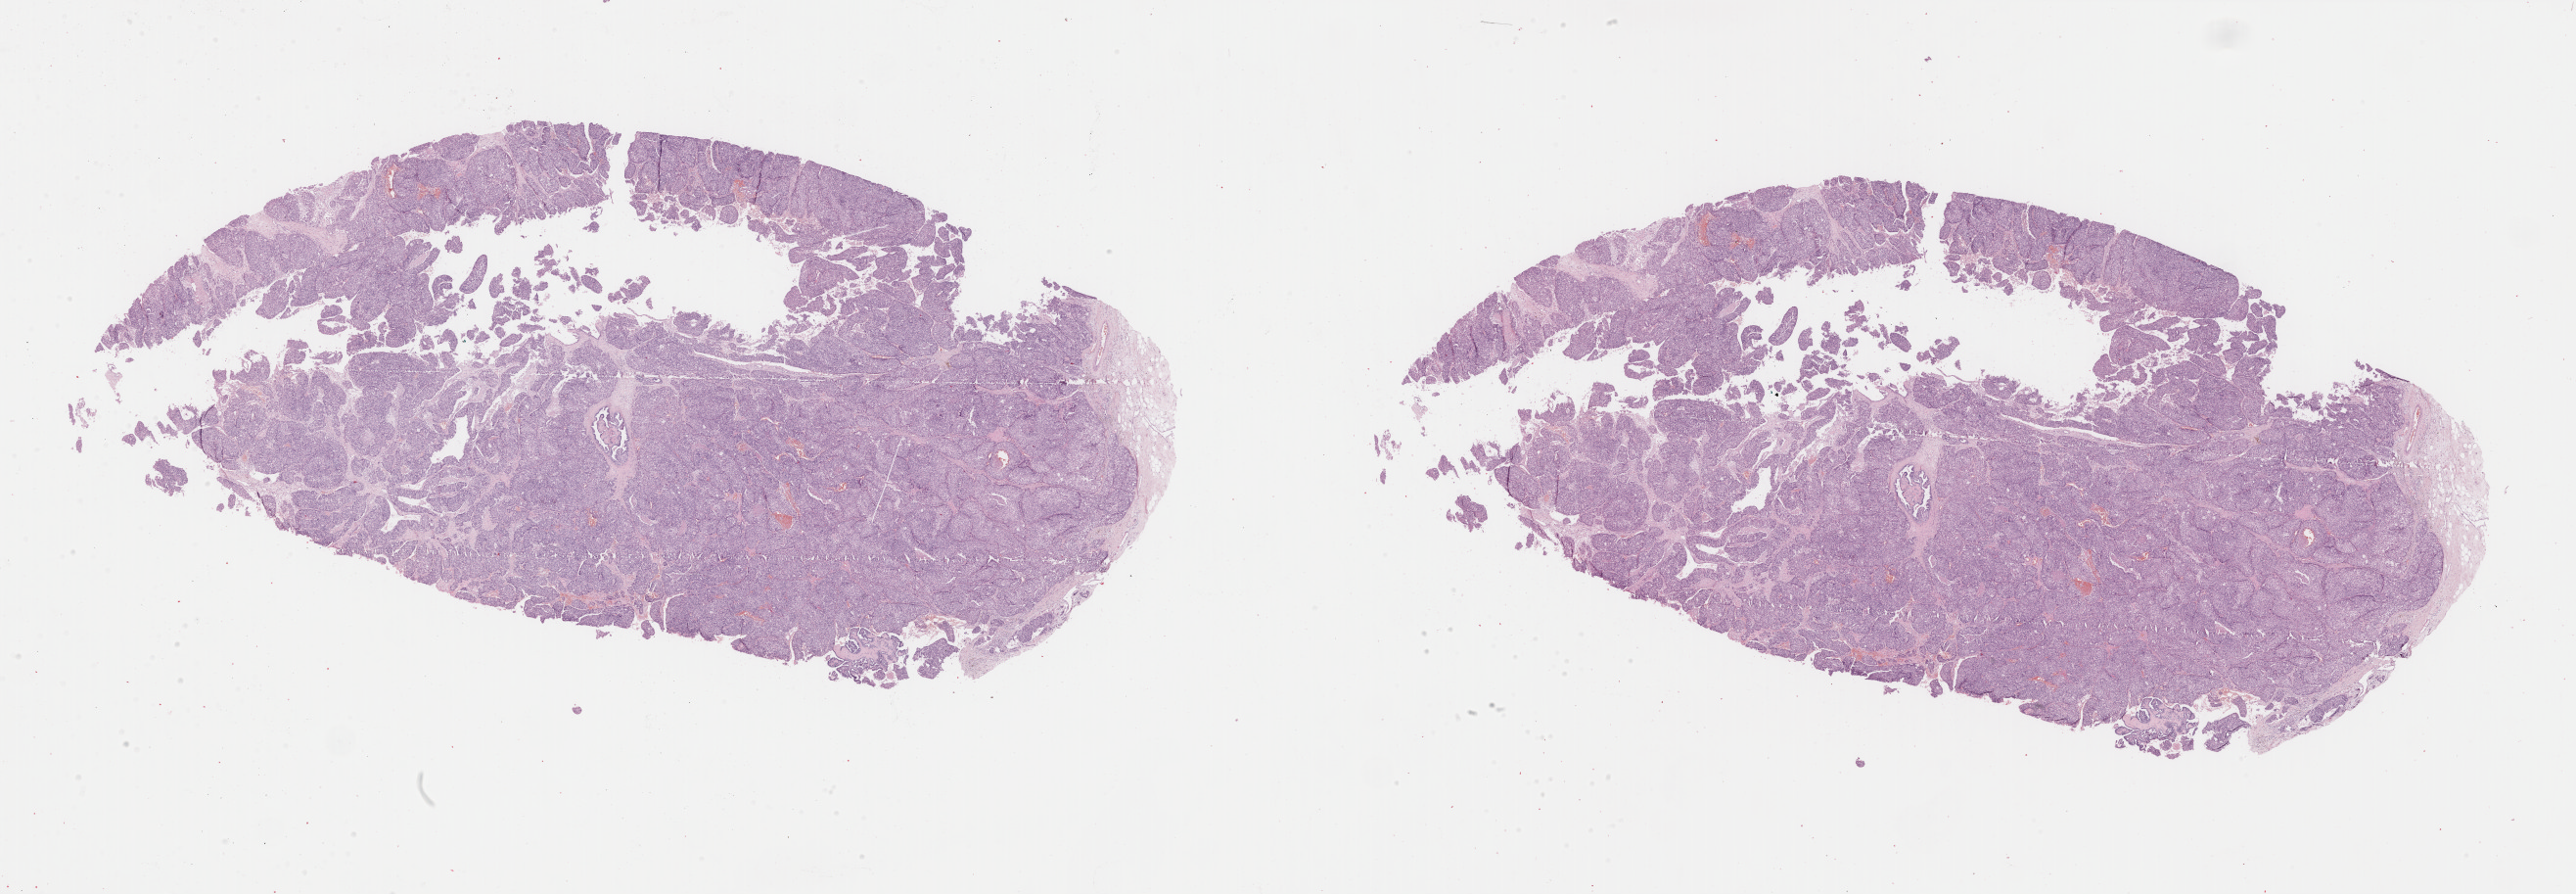
Digitized H&E tissue section (whole slide) — low-resolution overview of the scanned area, about 41.8 x 14.5 mm; formalin-fixed paraffin-embedded (FFPE) diagnostic section; sample: primary tumour, breast. Female, age 70 years at initial diagnosis.
Lymph nodes positive (case pathology): 0 of 15 examined. AJCC pathologic stage: IIA (7th edition). Pathologic diagnosis: Infiltrating duct mixed with other types of carcinoma.